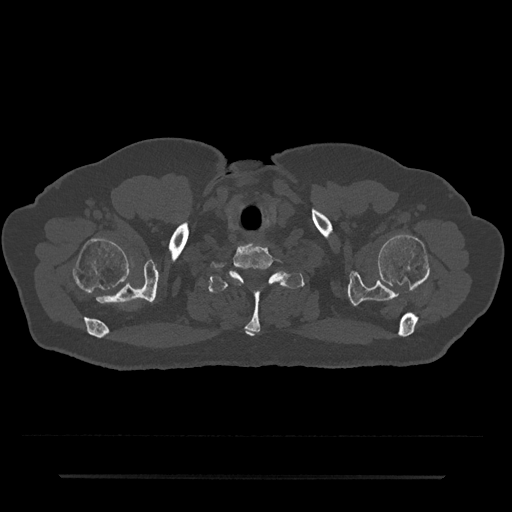
CT including the spine, one axial slice. Position 656 of 797 along the scan axis. Bone window (W 1800 / L 400 HU). 0.5 mm slice thickness. 512 × 512 image matrix, field of view 437 × 437 mm. Patient: male, 69 years. From the clinical record (not read from this slice): primary cancer: prostate.
Outlined on this slice (semi-automatic segmentation, software-assisted and operator-edited):
- T1 vertebra: bounding box <208,271,304,336> (left, top, right, bottom; pixels)